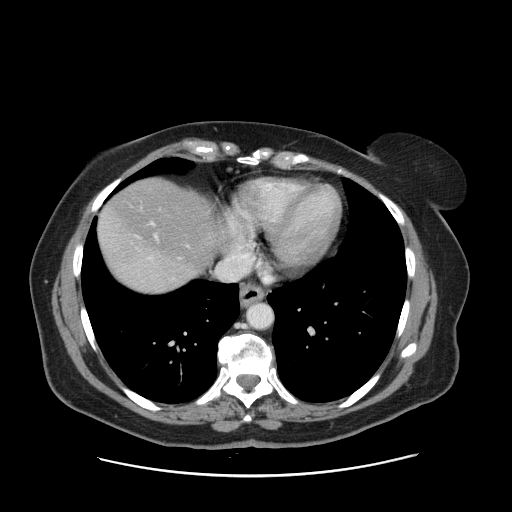
Contrast-enhanced abdominal CT, one axial slice. Intravenous contrast given. Soft-tissue window (W 400 / L 40 HU). 2.5 mm slice thickness. 512 × 512 image matrix, field of view 398 × 398 mm. Female patient, age 62 years. Case-level facts recorded for this patient, not image findings: diagnosis: colorectal cancer liver metastases, imaged before liver resection; multiple liver metastases: no.
Annotated regions visible in this slice (outlined manually by an expert reader):
- hepatic veins: bounding box (x1, y1, x2, y2) in pixels: (138, 235, 158, 259)
- liver: (98, 179, 216, 293)
- planned liver remnant (the part of the liver to remain after resection): (99, 179, 216, 272)